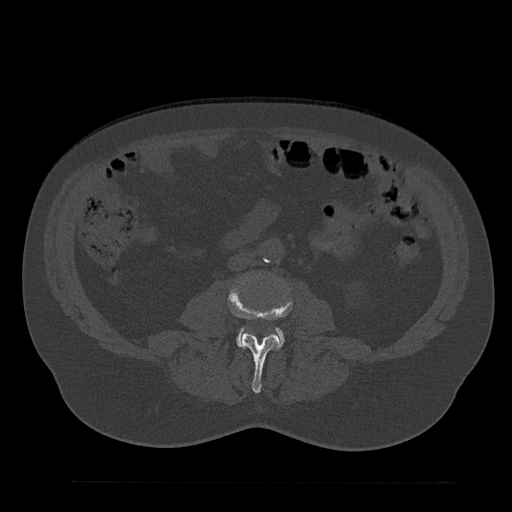
CT including the spine, one axial slice; position 10 of 797 along the scan axis; reconstruction kernel Br40s/3; 120 kVp; bone window (W 1800 / L 400 HU); 0.5 mm slice thickness; 512 × 512 image matrix, field of view 430 × 430 mm. Patient: male, 61 years. Case-level facts recorded for this patient, not image findings: primary cancer: prostate.
Outlined on this slice (semi-automatically segmented with operator editing):
- L3 vertebra: bounding box <228,274,292,393> (left, top, right, bottom; pixels)
- L4 vertebra: <237,329,284,346>